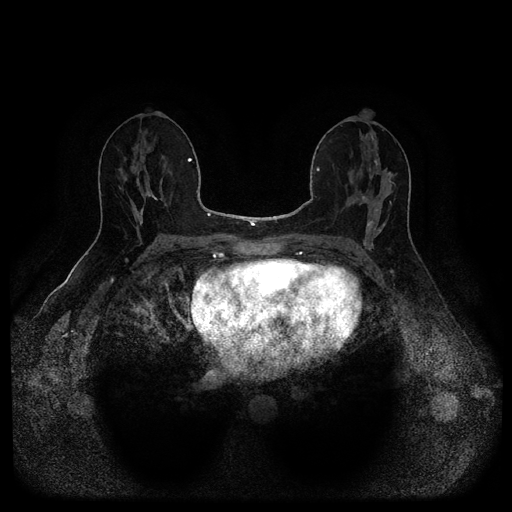
Breast MRI (dynamic contrast-enhanced, multi-phase), one axial slice; slice 57 of 116 in the series (ordered by position); dynamic contrast-enhanced series, time point 2 of 5 at this slice position (early post-contrast); 1.5 T; TE 2.6 ms, TR 5.3 ms; 2.2 mm slice thickness; 512 × 512 image matrix, field of view 350 × 350 mm. Patient: female, 49 years.
Annotated regions visible in this slice (semi-automatic segmentation, software-assisted and operator-edited):
- breast lesion (labelled benign in the annotation): box from (x=366, y=216) to (x=378, y=234) px